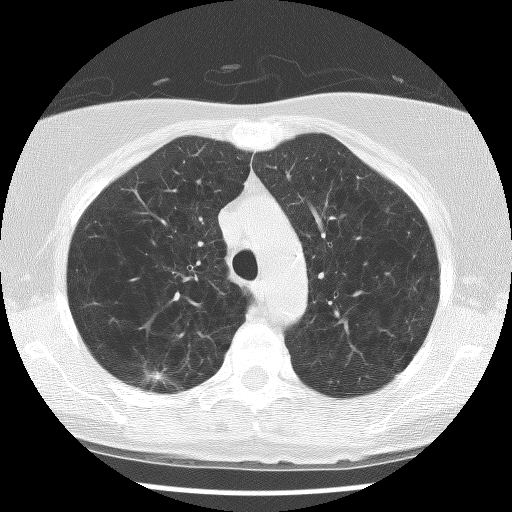
Axial slice from a low-dose chest CT screening exam; first (baseline) screen; lung window (W 1500 / L -600 HU); 120 kVp. Female participant, aged 63 years at enrolment. Former smoker at enrolment.
Lesion marked by an expert reader, box from (x=128, y=354) to (x=188, y=404) px. Screening reader's record for this exam (one nodule recorded; not confirmed to be the boxed lesion): non-calcified nodule or mass ≥4 mm, right upper lobe, 9 × 6 mm, spiculated (stellate) margins, mixed attenuation. Official screen result: positive, change unspecified: nodule(s) >= 4 mm or enlarging nodule(s), mass(es), or other non-specific abnormalities suspicious for lung cancer.